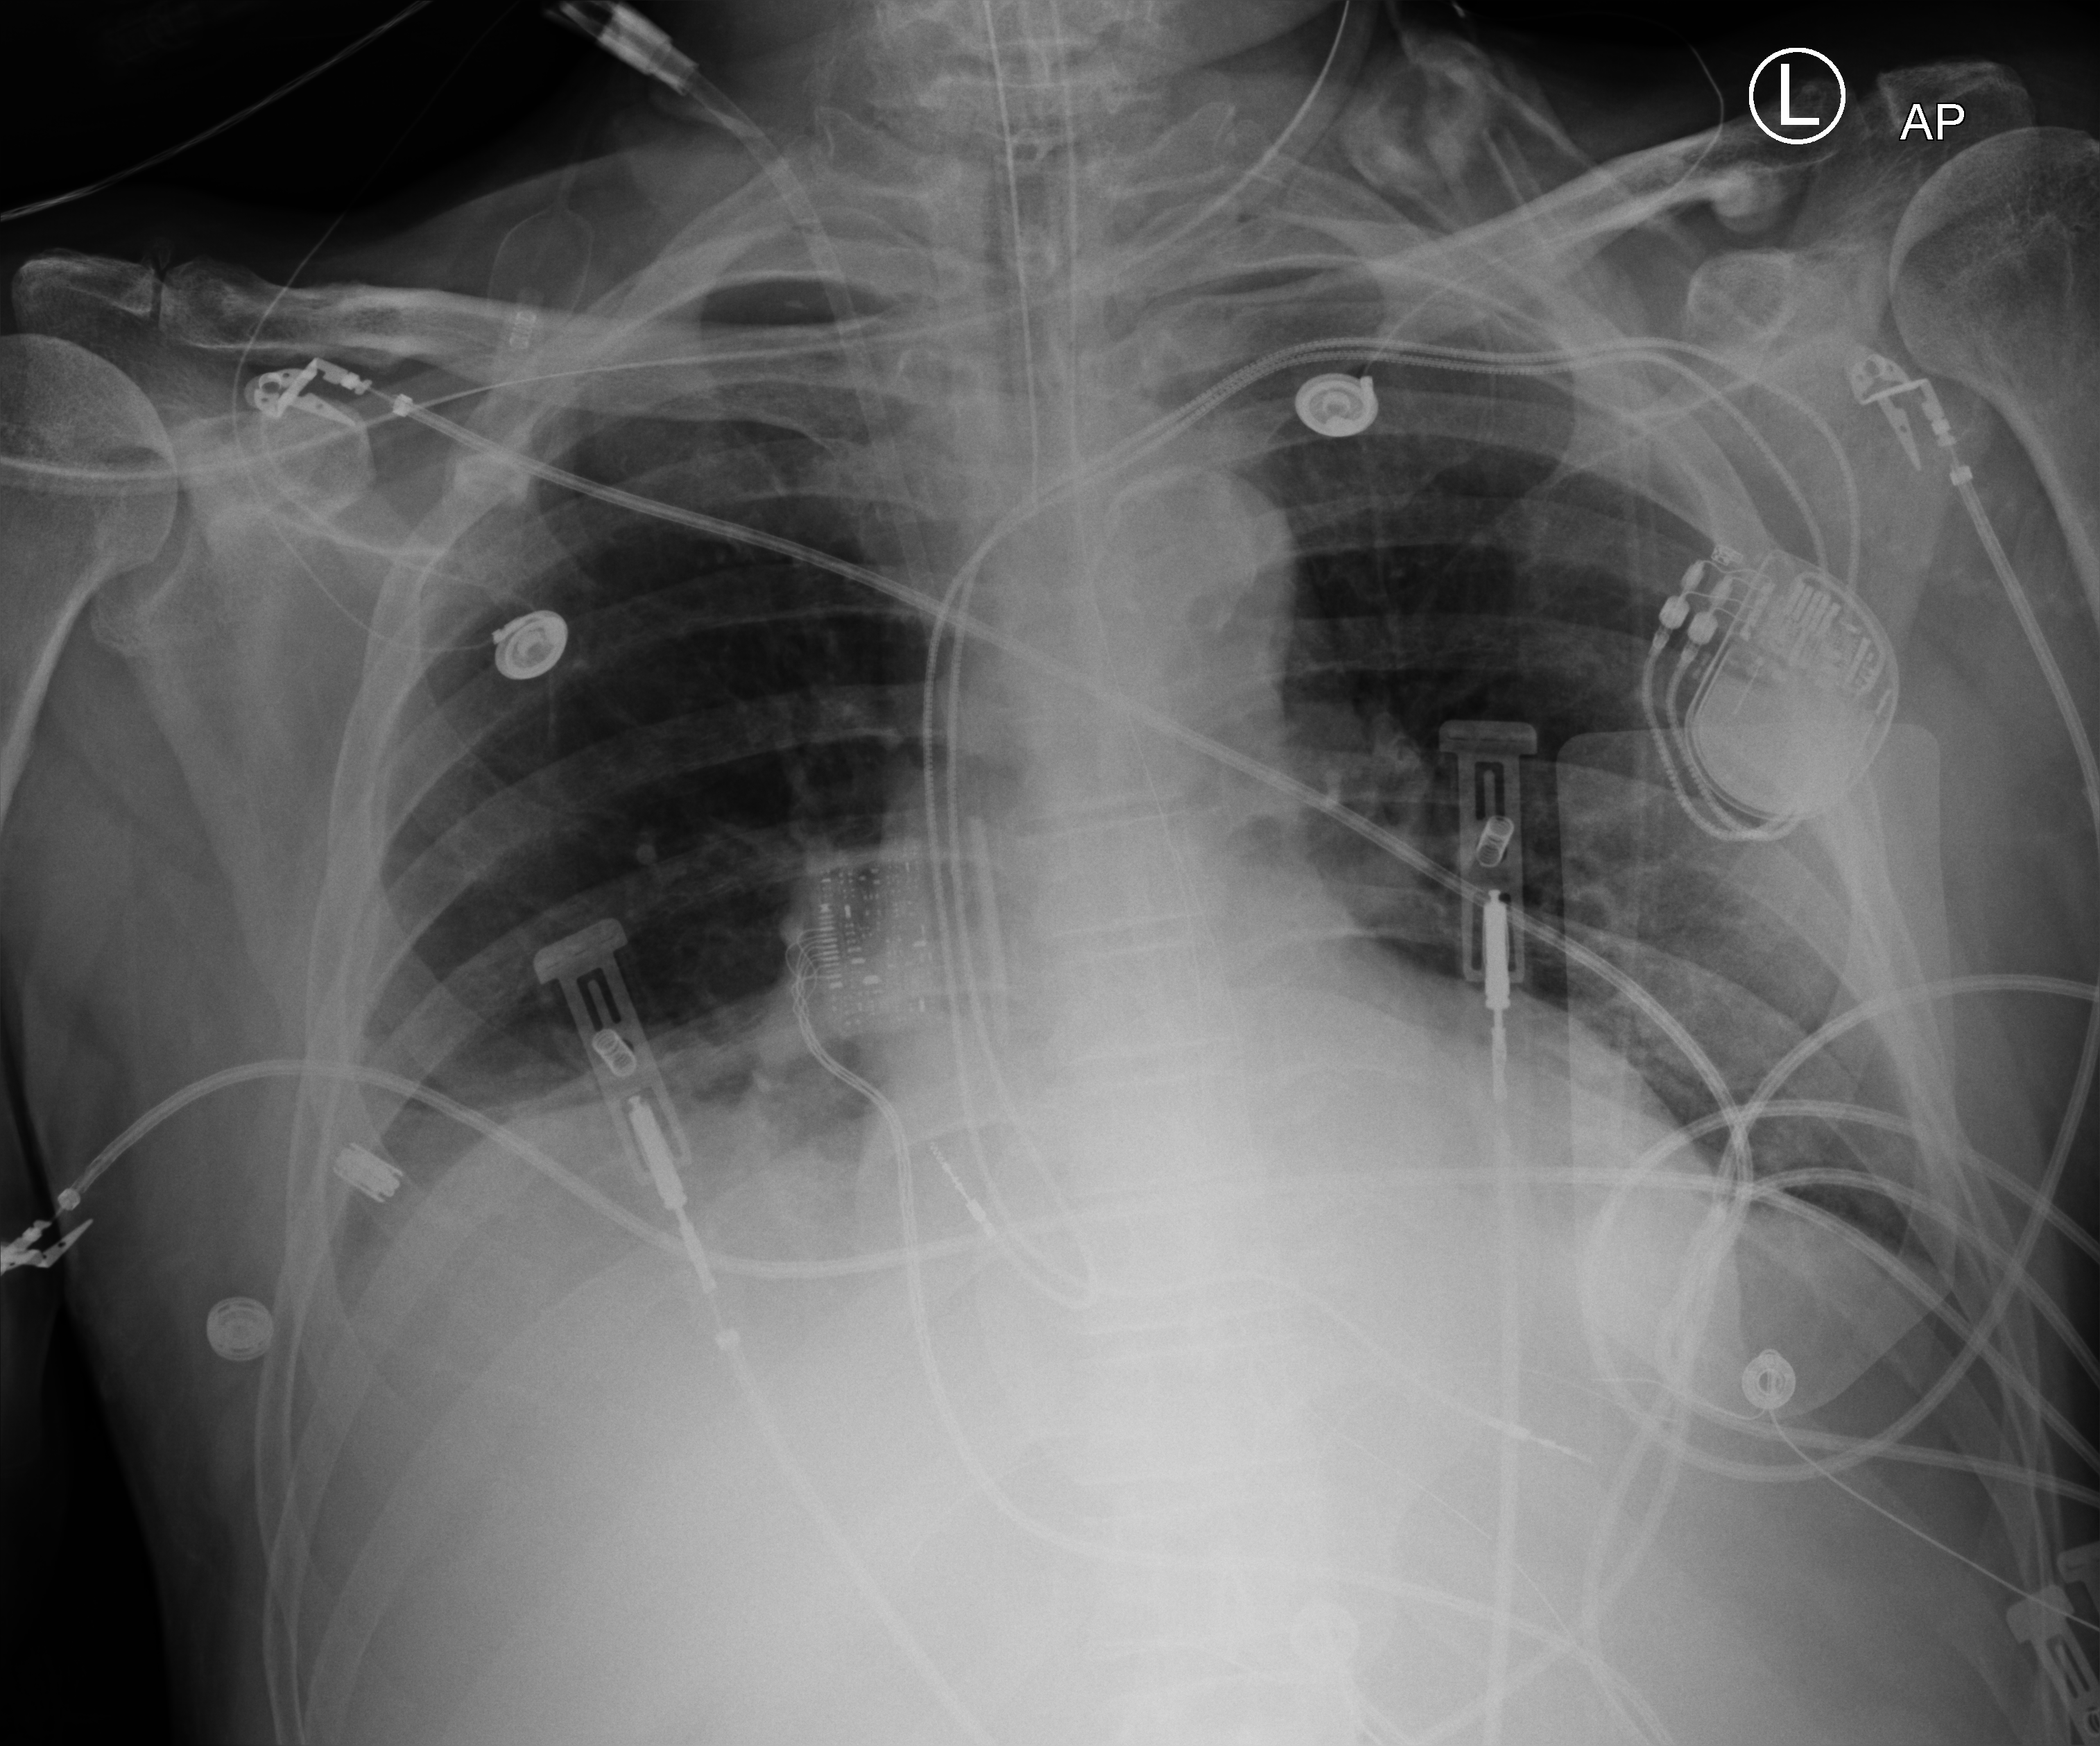
Bedside chest radiograph (computed radiography), anteroposterior (AP) projection. Patient hospitalised with COVID-19; male, aged 60–74 years.
Admission-level facts for this patient (not findings on this image; timing relative to this image not recorded): mechanically ventilated during this hospital stay: yes; admitted to intensive care during this hospital stay: yes; length of hospital stay: 41 days.